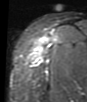
MRI of an extremity soft-tissue mass, one axial slice; position 34 of 48 along the scan axis; STIR; MR volume resampled by the dataset authors to the PET/CT grid (not the native acquisition matrix); 87 × 102 image matrix, field of view 85 × 100 mm. Female patient. Case-level facts recorded for this patient, not image findings: histological type: synovial sarcoma; grade: intermediate; site of the primary tumour: right thigh.
Structures marked on this image (expert contour drawn on MRI and transferred to this co-registered scan by the dataset authors):
- gross tumour volume including surrounding oedema: bounding box (x1, y1, x2, y2) in pixels: (31, 40, 48, 66)
- gross tumour volume (mass): (31, 45, 45, 66)